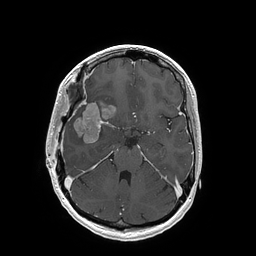
Brain MRI from a brain-tumour surgery series, one axial slice. Slice 109 of 202 in the series (ordered by position). T1-weighted post-contrast. 1 mm slice thickness. 256 × 256 image matrix. Case-level facts recorded for this patient, not image findings: histopathology: Glioblastoma; WHO grade: 4; IDH mutation: no; tumour location: Right Insular.
Outlined on this slice (manually delineated by an expert):
- tumour: box from (x=74, y=103) to (x=116, y=144) px